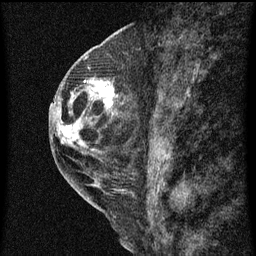
Breast MRI (dynamic contrast-enhanced), one sagittal slice; position 25 of 60 along the scan axis; dynamic contrast-enhanced series, image 2 of 3 at this slice position (ordered by acquisition); 1.5 T; TE 4.2 ms, TR 8 ms; 2 mm slice thickness; 256 × 256 image matrix, field of view 180 × 180 mm. Patient: female, 48 years.
Annotated regions visible in this slice (semi-automatically segmented with operator editing):
- analysis volume of interest (the breast-tissue region the enhancement analysis was run in; not a lesion): bounding box [x1, y1, x2, y2] px = [89, 78, 123, 113]
- tumour enhancement mask (voxels above the 70 % enhancement threshold inside the analysis volume of interest): [93, 80, 116, 113]